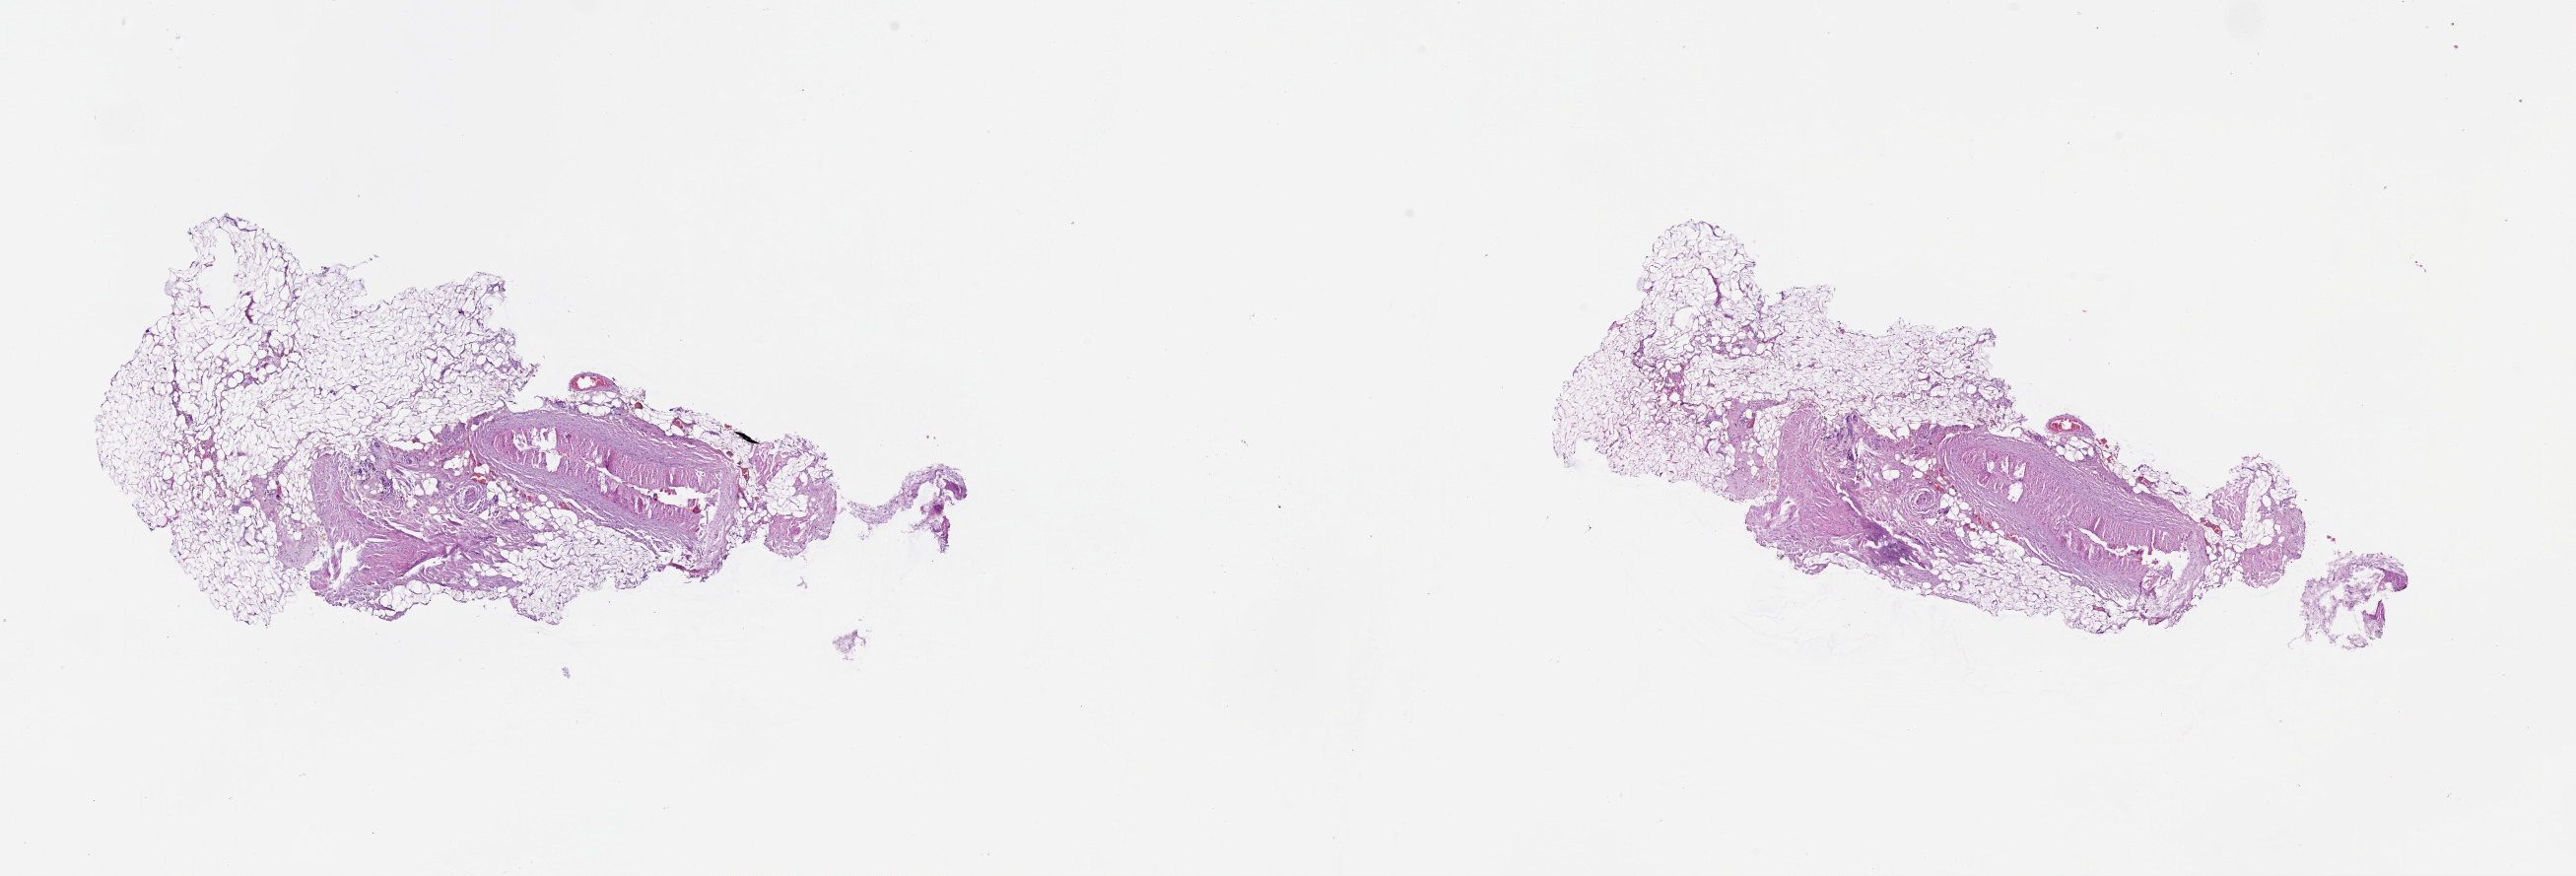
Whole-slide histology image, Hematoxylin and eosin (H&E) stained, low-resolution overview of the scanned area, about 21.0 x 7.2 mm (slide scanned at 20x). Male, 72 y/o.
- patient diagnosis: Malignant melanoma, NOS